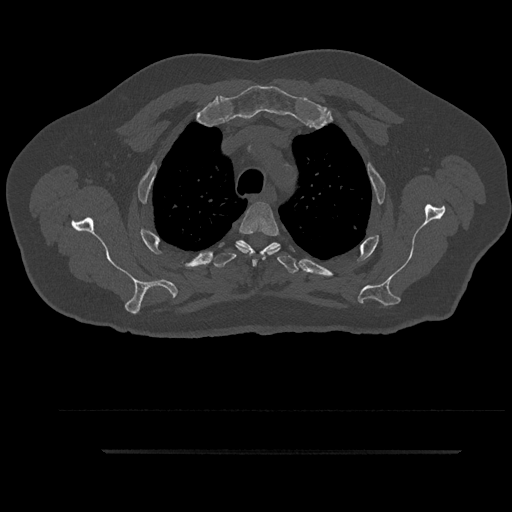
CT including the spine, one axial slice. Slice 701 of 797 in the series (ordered by position). Bone window (W 1800 / L 400 HU). 512 × 512 image matrix. Patient: male, 63 years. From the clinical record (not read from this slice): primary cancer: renal; vertebrae with lytic lesions (as recorded): T8.
Annotated regions visible in this slice (semi-automatically segmented with operator editing):
- T3 vertebra: bounding box (x1, y1, x2, y2) in pixels: (236, 201, 280, 265)
- T4 vertebra: (211, 240, 299, 274)